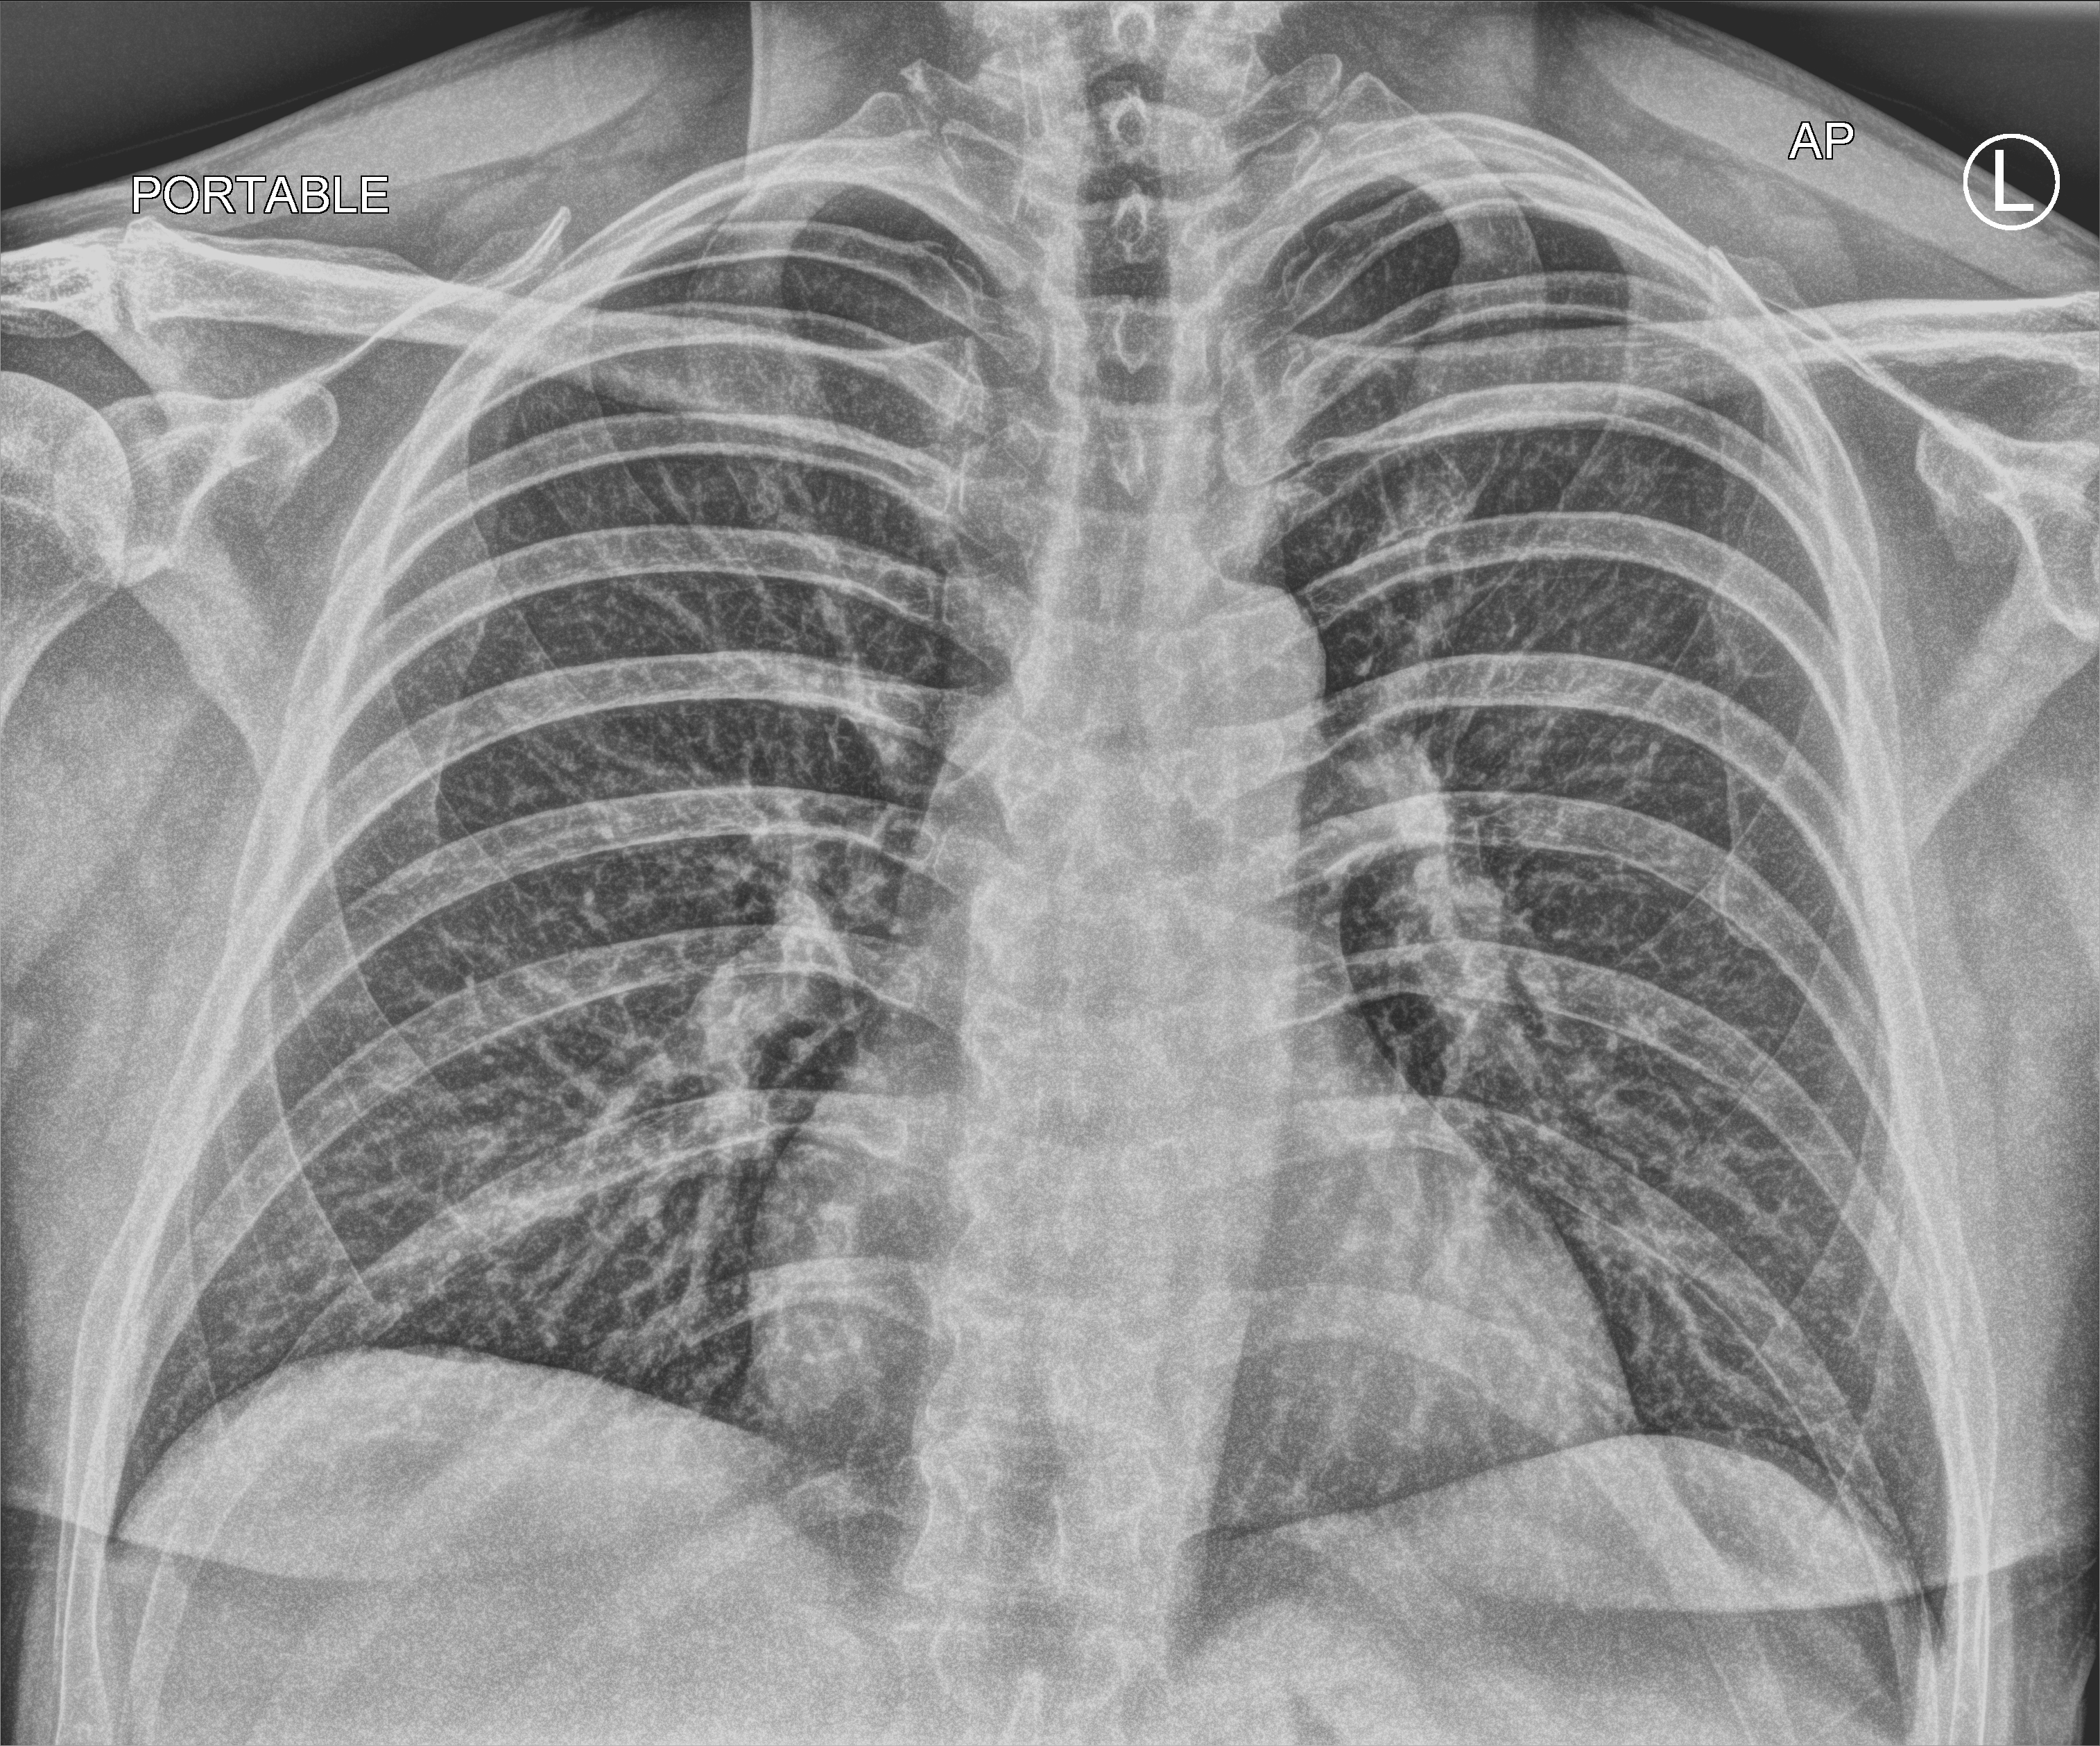
Portable chest radiograph; anteroposterior (AP) projection. Male patient hospitalised with COVID-19, age 18–59 years.
Admission-level facts for this patient (not findings on this image; timing relative to this image not recorded):
- admitted to intensive care during this hospital stay: no
- length of hospital stay: 1 day